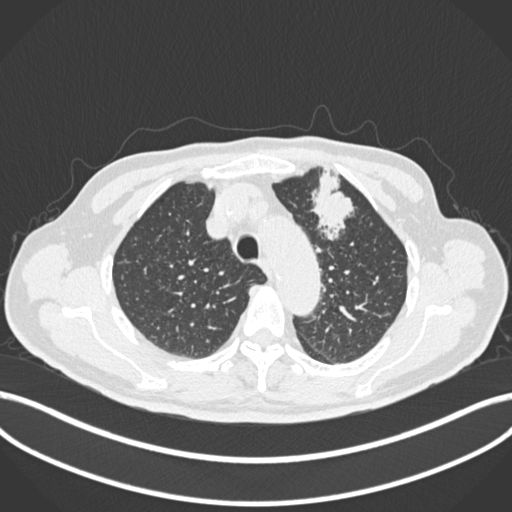
Chest CT, one axial slice. Position 199 of 261 along the scan axis. Reconstruction kernel B30f. 120 kVp. Lung window (W 1500 / L -600 HU). 1 mm slice thickness. 512 × 512 image matrix. Male patient, age 74 years. From the clinical record (not read from this slice): clinical TNM (as recorded): T2b N0 M1c.
Annotated regions visible in this slice (bounding box drawn by a radiologist):
- lung tumour (recorded histology: adenocarcinoma): box from (x=305, y=164) to (x=365, y=246) px